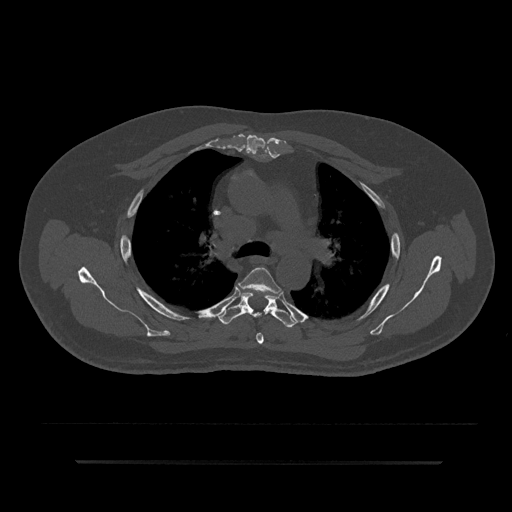
CT including the spine, one axial slice. Position 593 of 797 along the scan axis. 120 kVp. Bone window (W 1800 / L 400 HU). 0.5 mm slice thickness. 512 × 512 image matrix. Male patient, age 59 years. From the clinical record (not read from this slice): primary cancer: bile ducts; vertebrae with lytic lesions (as recorded): T10.
Structures marked on this image (semi-automatically segmented with operator editing):
- T4 vertebra: bounding box [x1, y1, x2, y2] px = [238, 267, 281, 344]
- T5 vertebra: [219, 292, 298, 327]